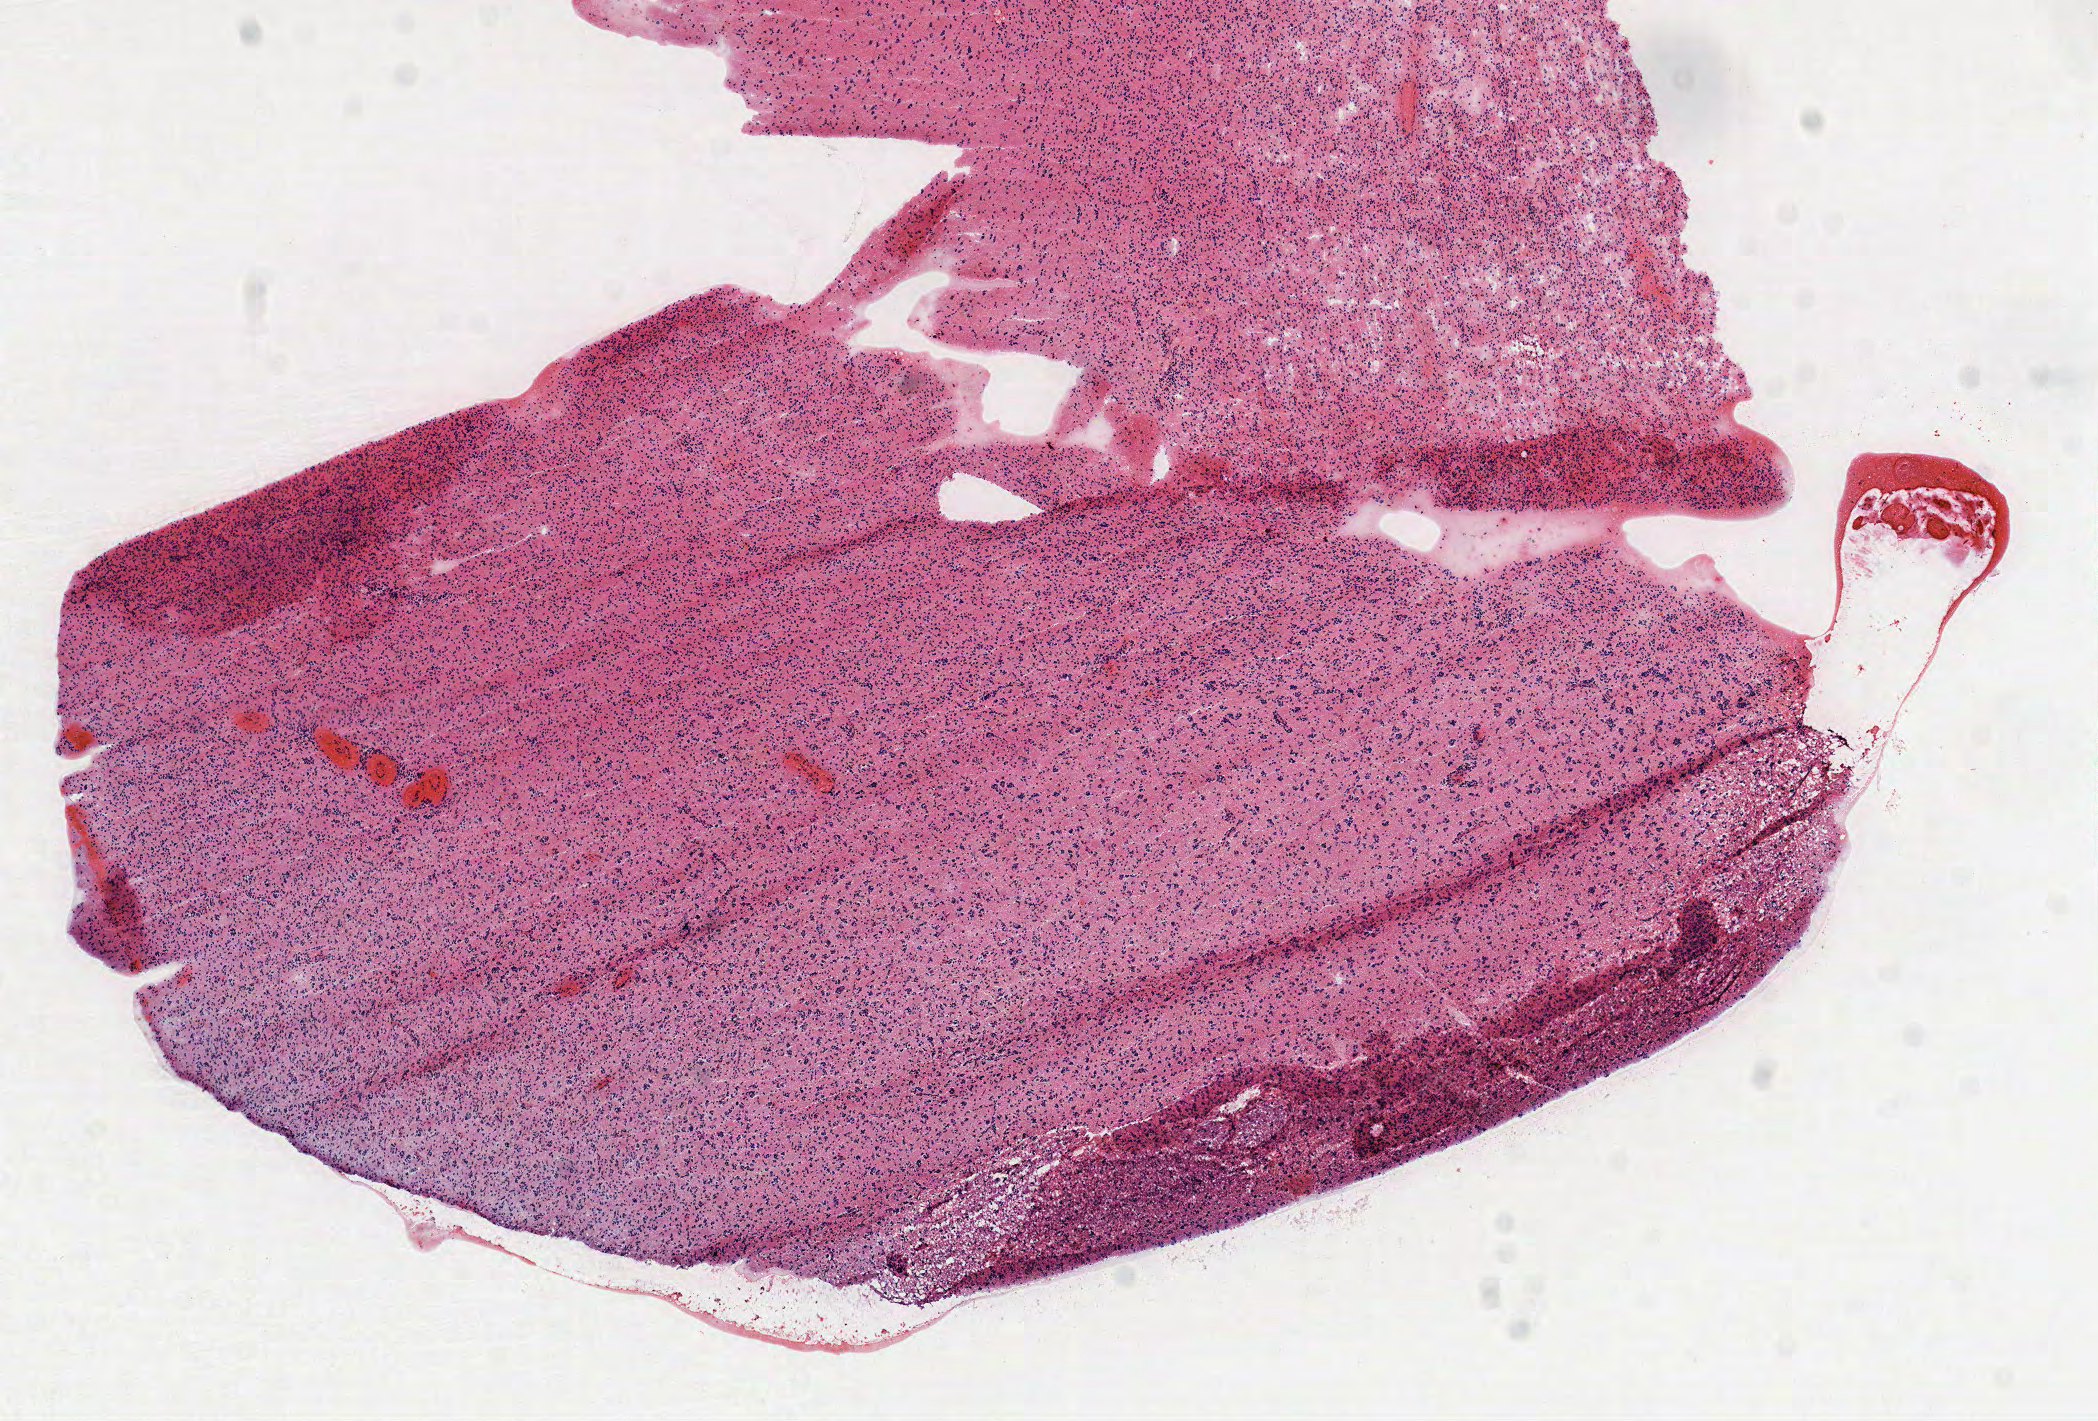
Digitized Hematoxylin and eosin (H&E) stained tissue section (whole slide), whole scanned area (about 8.5 x 5.7 mm, slide scanned at 40x) shown as a low-resolution overview. Frozen section from the top of the tissue portion. Sample: primary tumour, brain. Patient: male, age at initial diagnosis 39 years.
Histologic diagnosis: Oligodendroglioma, NOS.